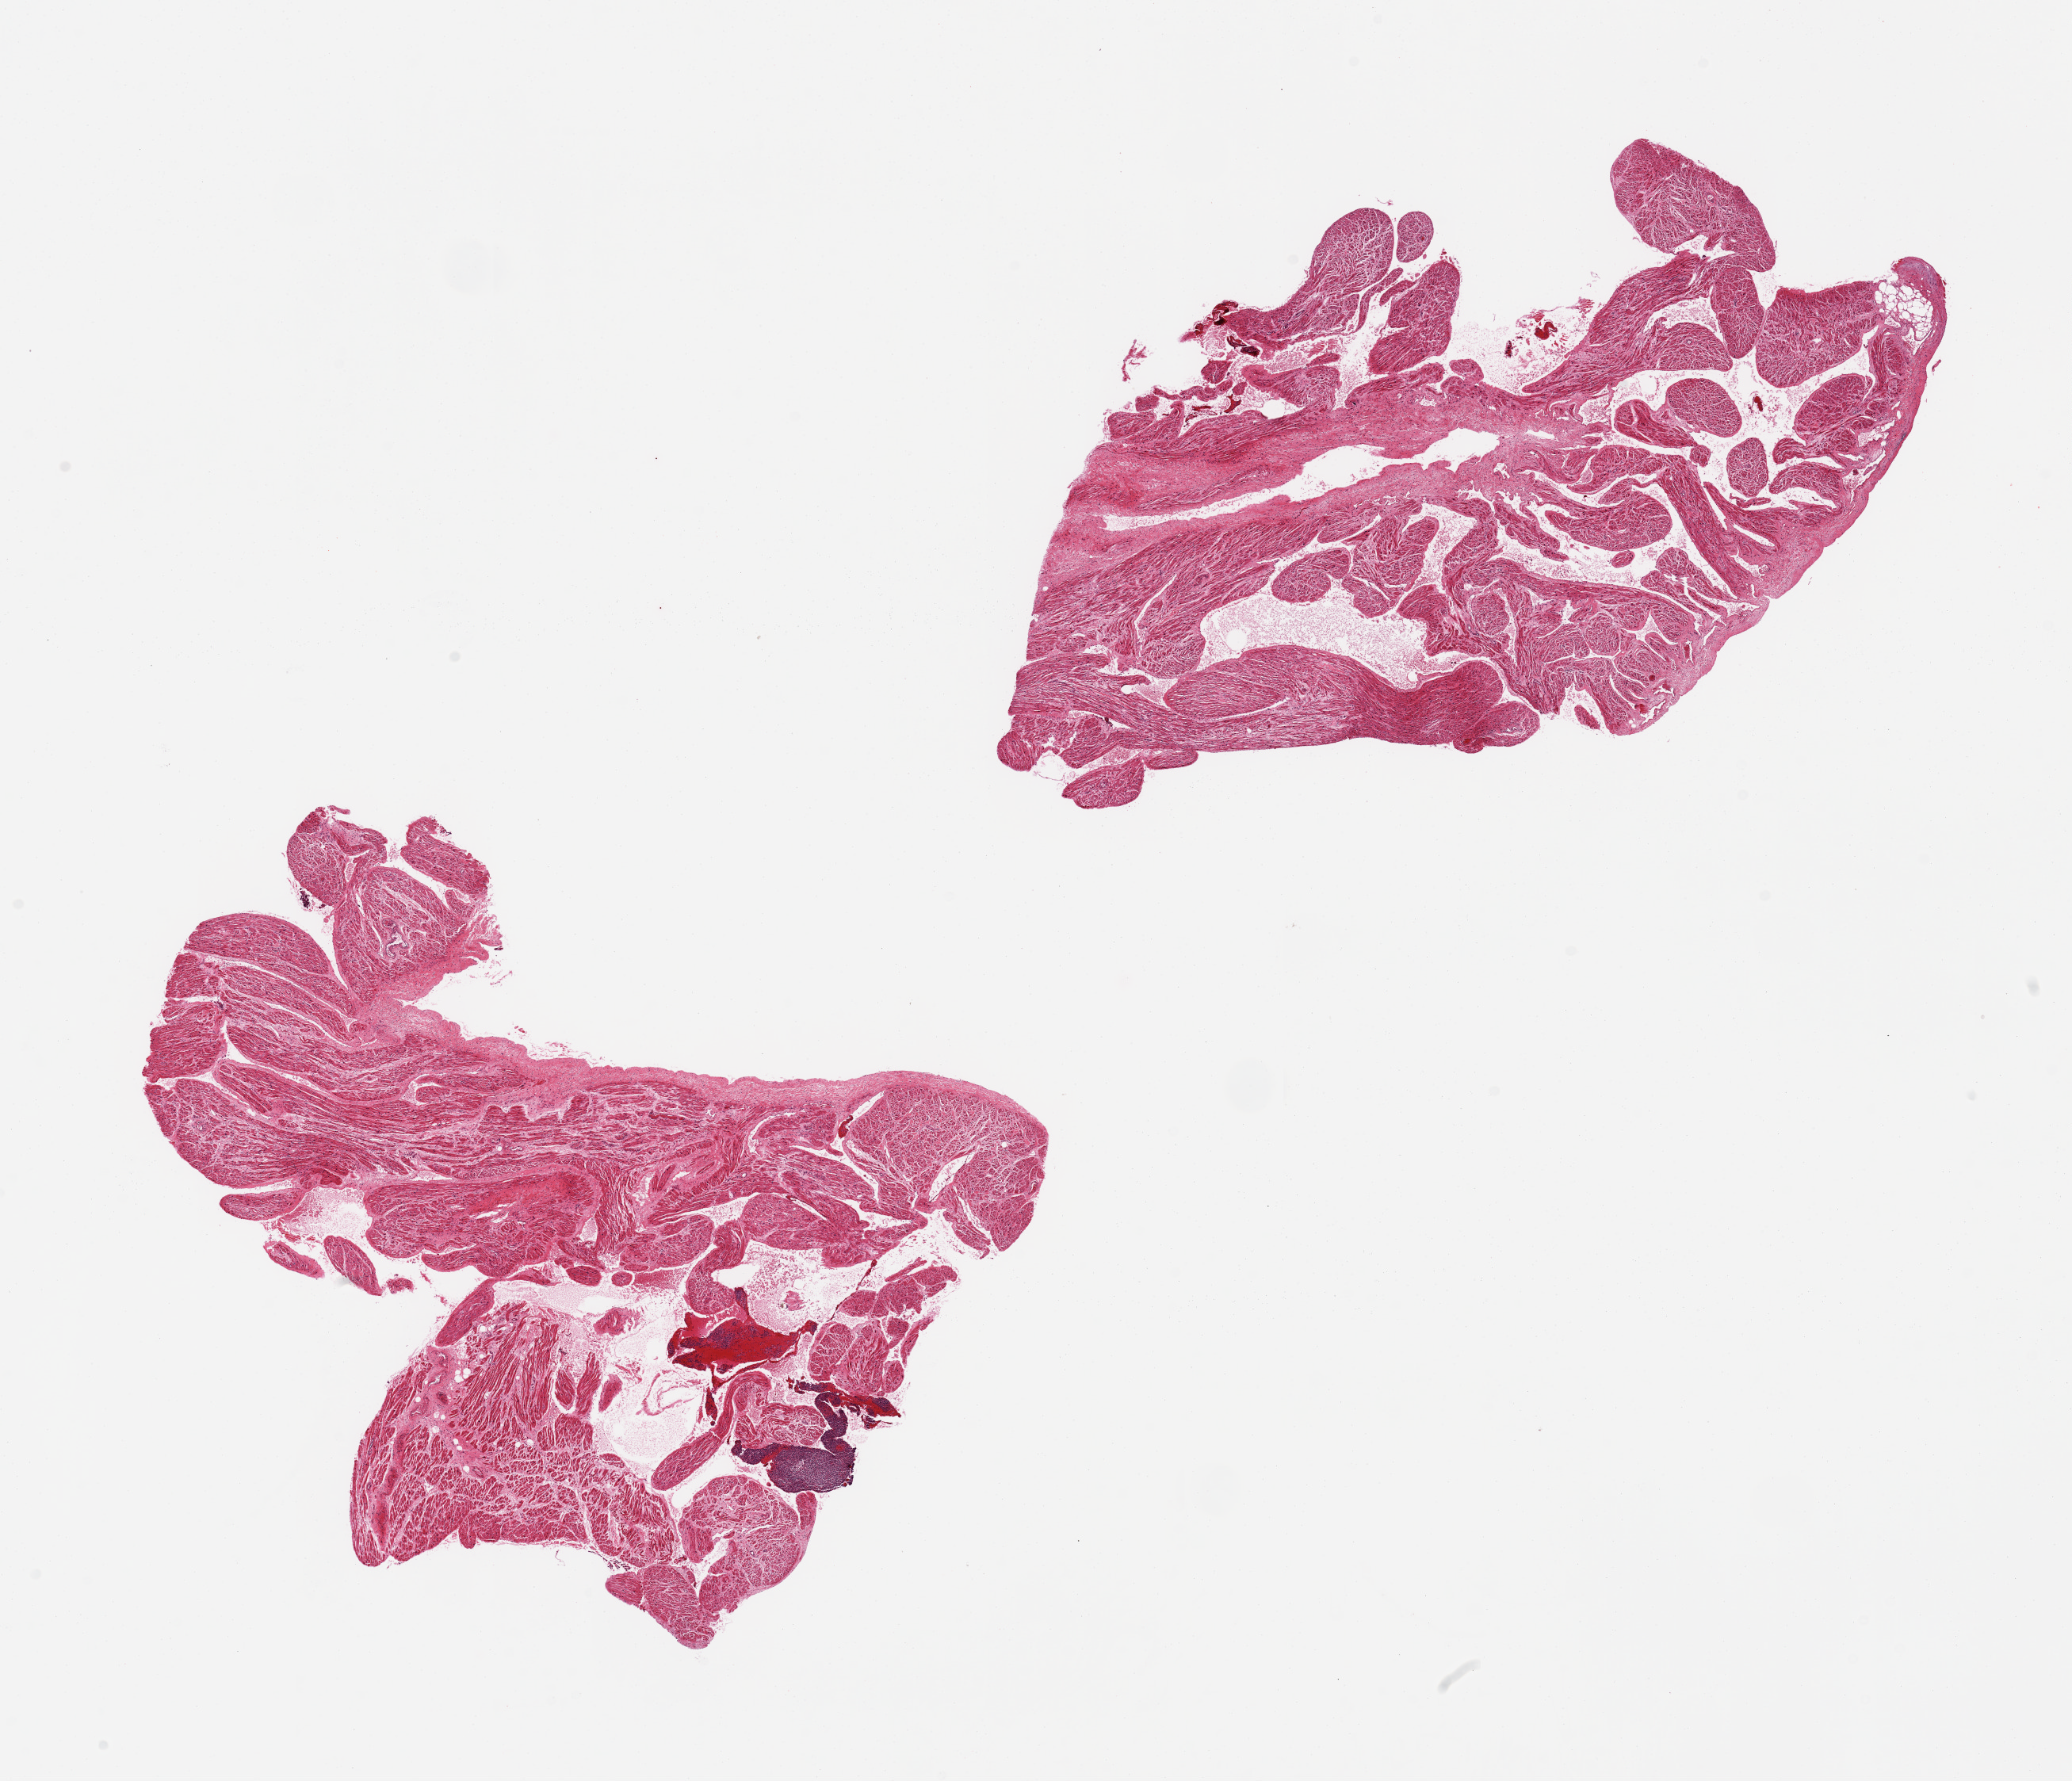
Whole-slide image, hematoxylin and eosin (H&E) stain — low-resolution overview of the scanned area, about 20.7 x 17.8 mm; PAXgene-fixed paraffin-embedded (PFPE) section; section of auricular appendage (target tissue); donor tissue sample. Female donor.
Reviewer comment on this tissue sample: 2 pieces, no abnormalities; incedental 'contaminating' fragment of lymph node ? mediastinal.